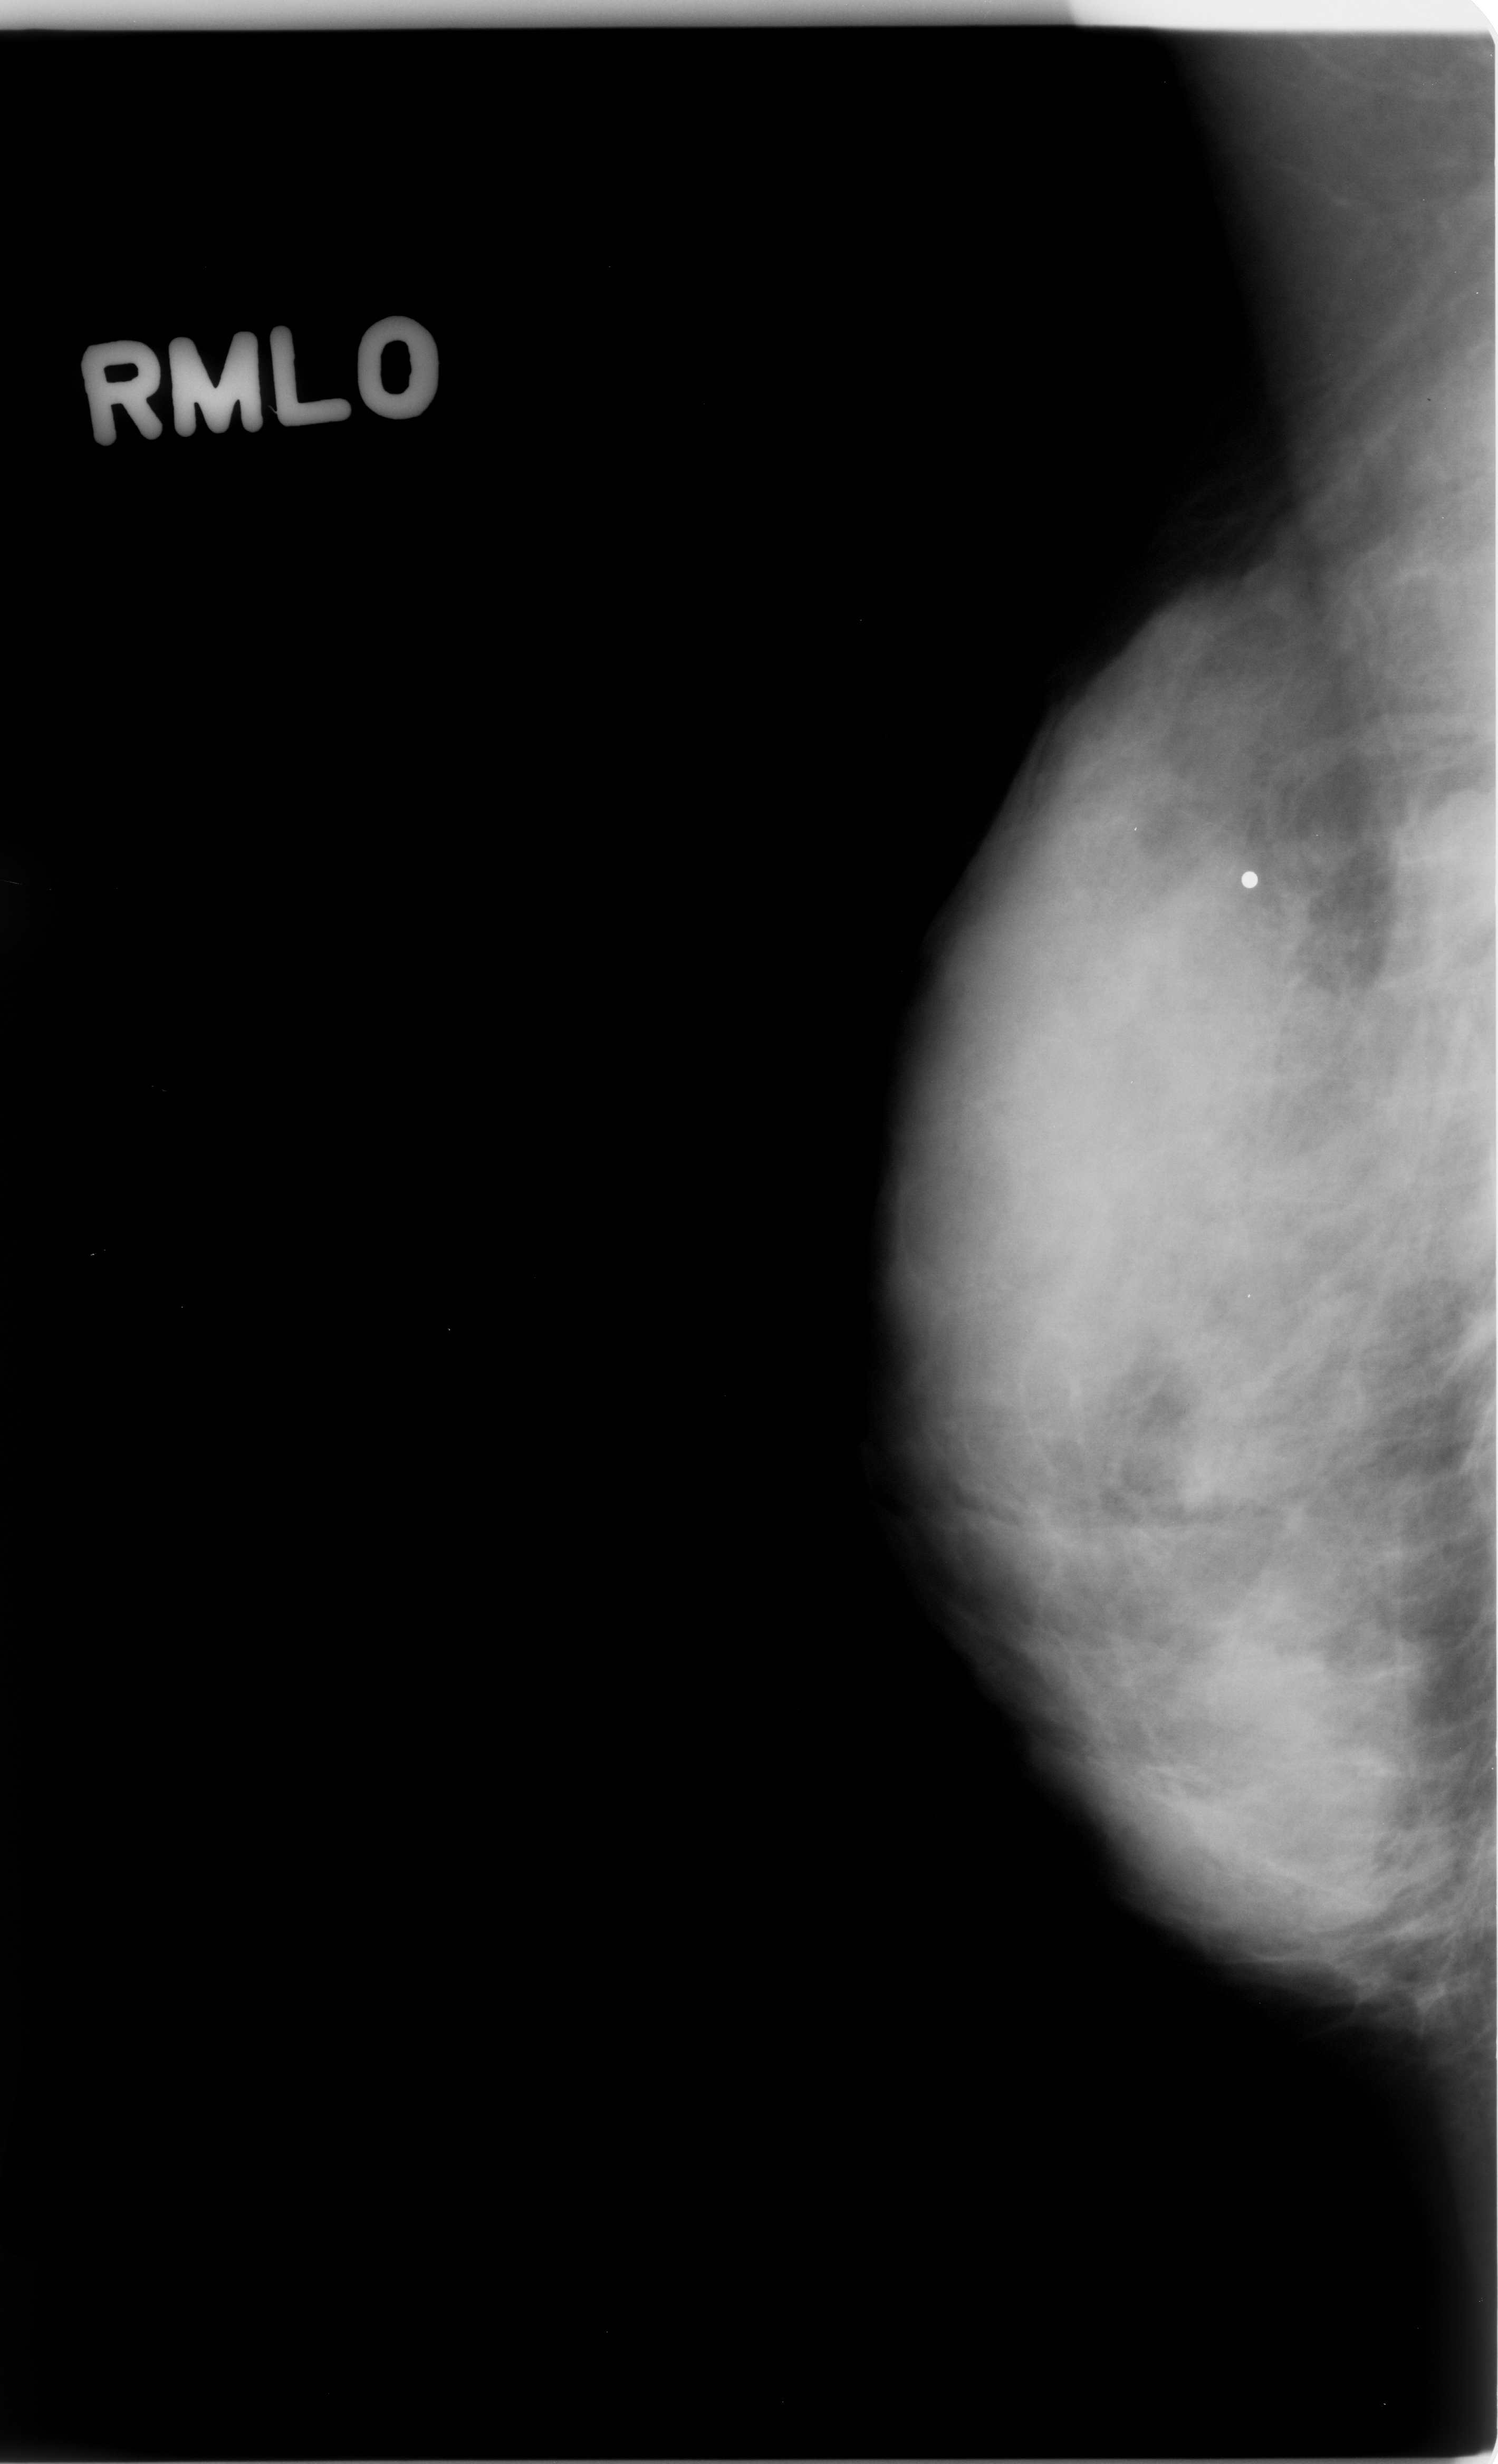
Digitized screen-film mammogram; right breast; mediolateral oblique (MLO) view; breast composition: extremely dense (BI-RADS density category 4 of 4); 1498 × 2464 image matrix.
Marked abnormalities (boxes around the expert regions of interest):
- mass, shape oval, margins obscured; BI-RADS assessment category 4; subtlety rating 4 on a 1 (subtle) to 5 (obvious) scale; pathology (as recorded): benign: box from (x=1375, y=801) to (x=1484, y=966) px